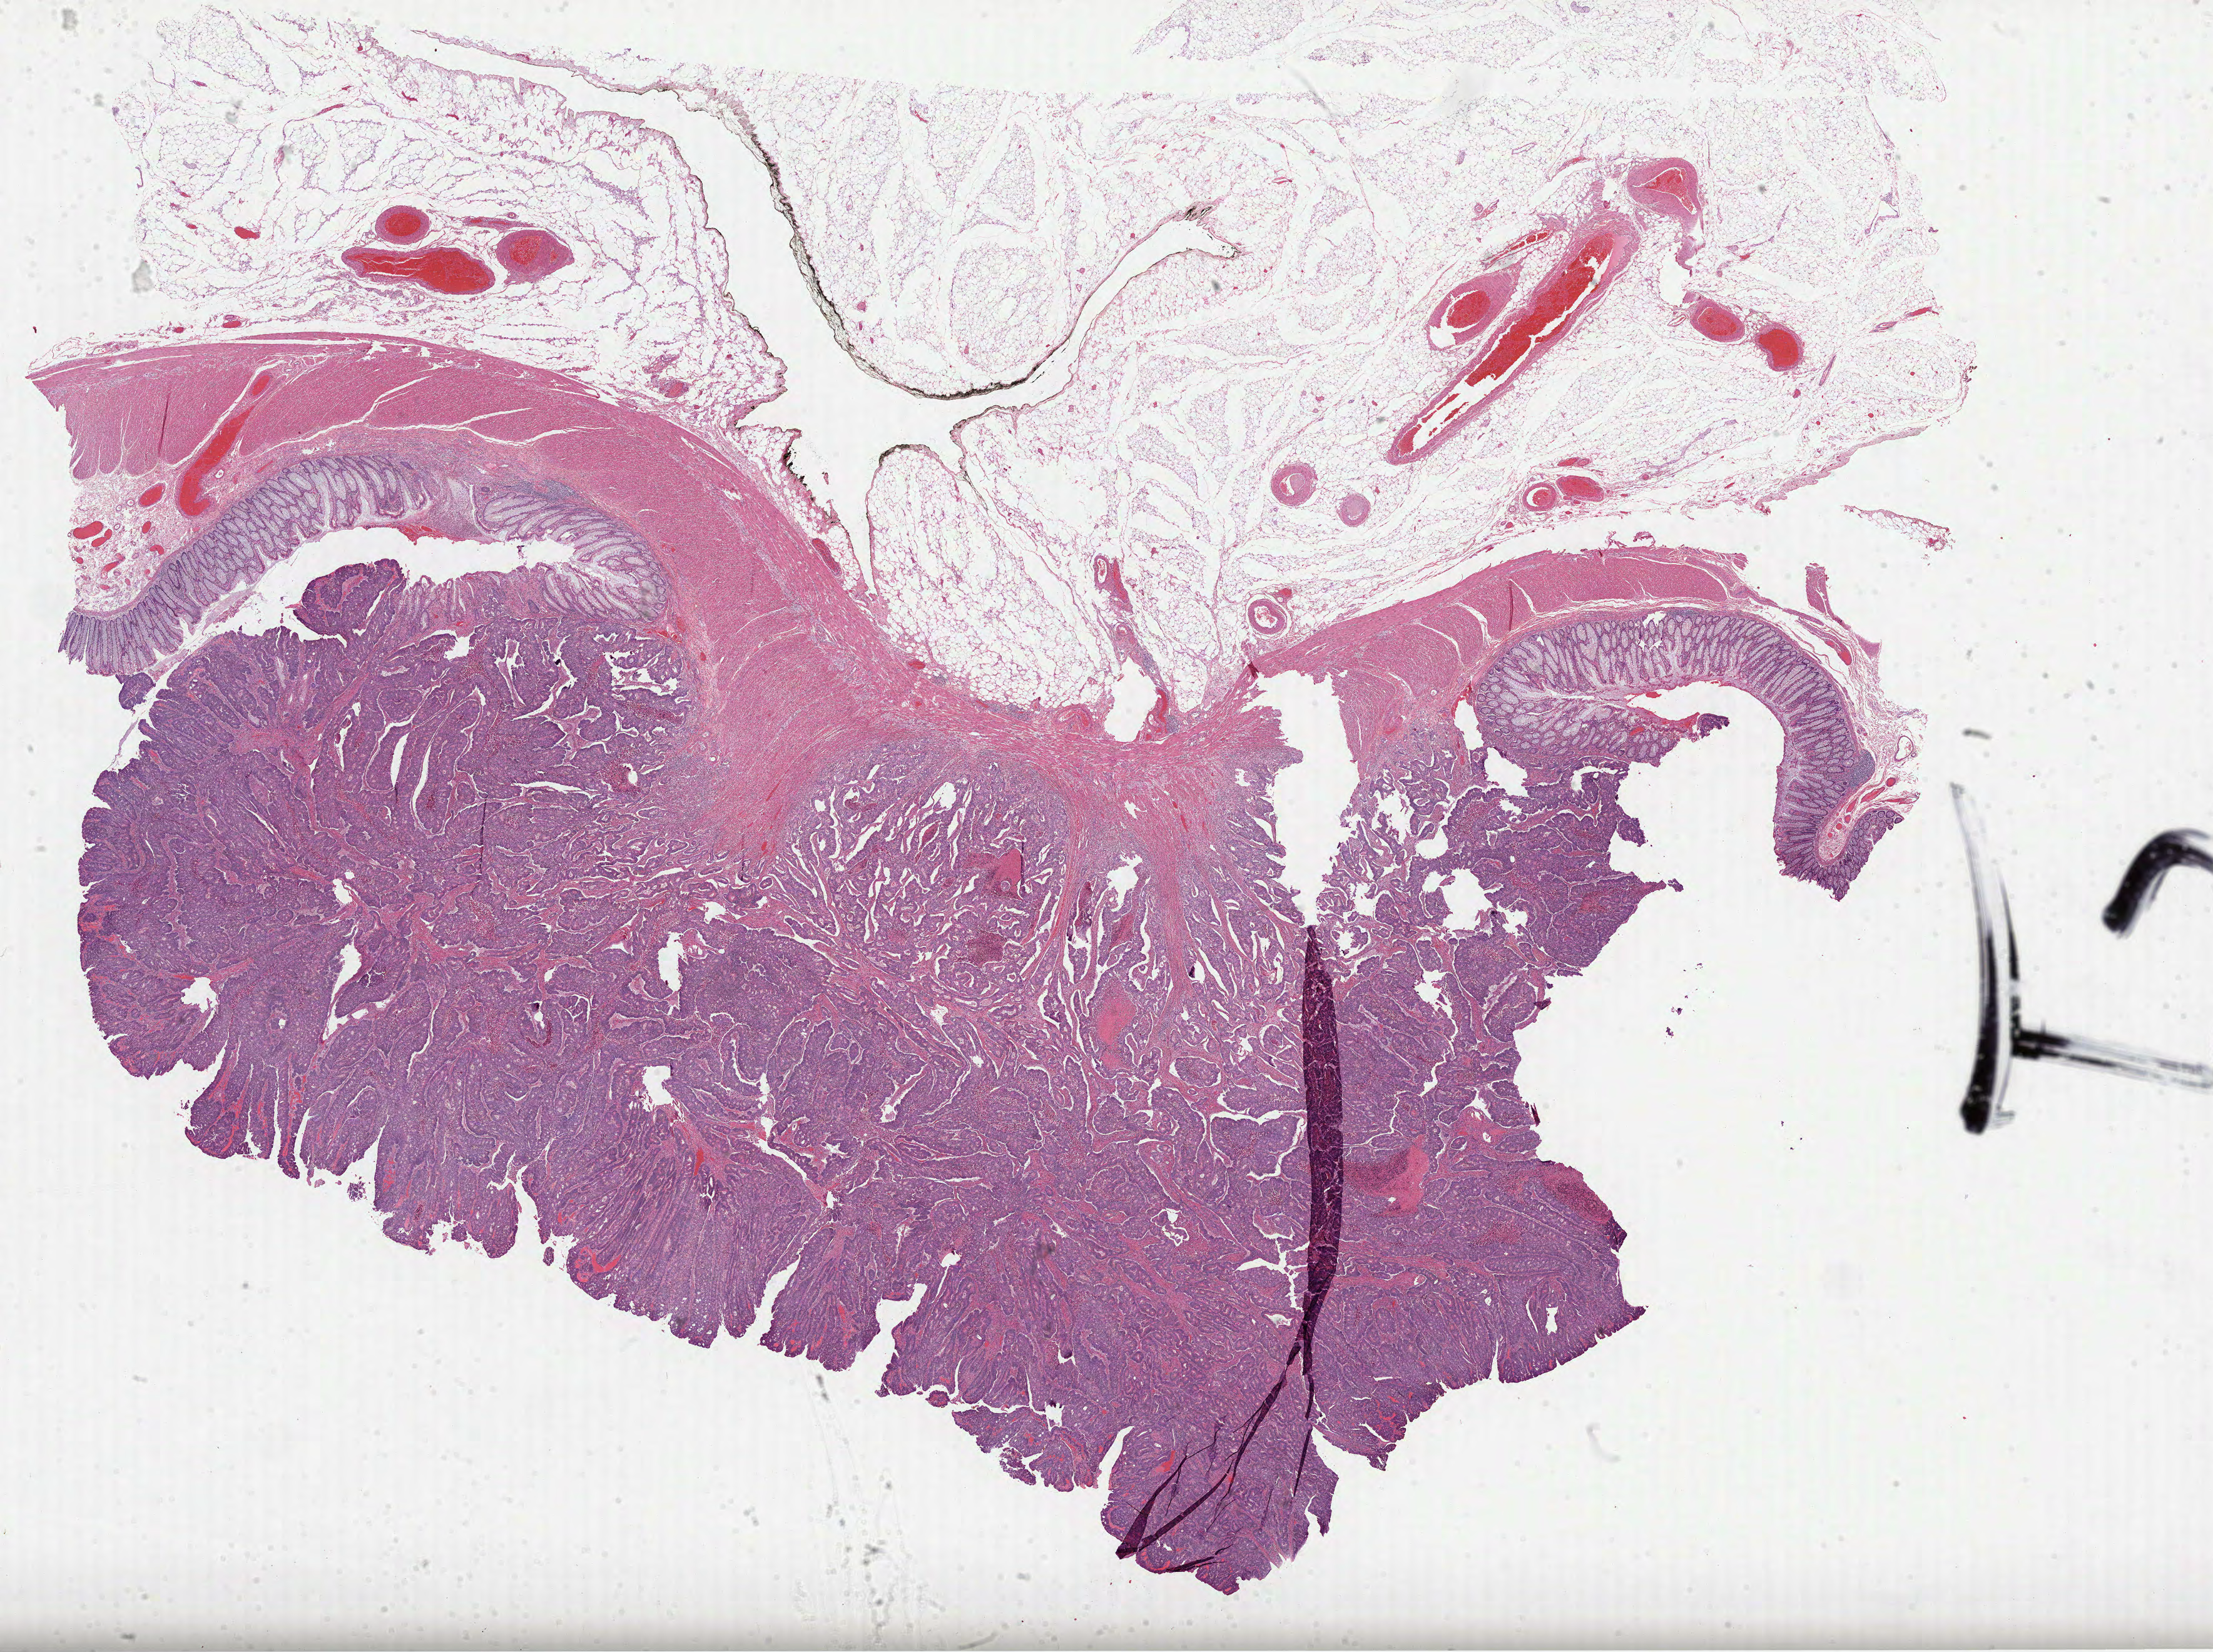
Whole-slide histology image, H&E-stained, low-resolution overview of the scanned area, about 28.5 x 21.3 mm; formalin-fixed paraffin-embedded (FFPE) diagnostic section; sample: primary tumour, colon. Female patient; age at initial diagnosis 55 years.
• lymph nodes positive (case pathology): 2 of 12 examined
• AJCC pathologic stage: IIIA (6th edition)
• histologic diagnosis: Adenocarcinoma, NOS (sigmoid colon)